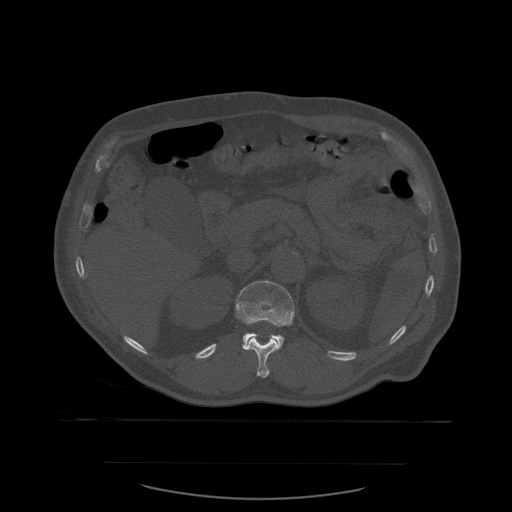
CT including the spine, one axial slice. Position 260 of 590 along the scan axis. Bone window (W 1800 / L 400 HU). 512 × 512 image matrix, field of view 479 × 479 mm. Patient age 71 years. From the clinical record (not read from this slice): primary cancer: lung.
Annotated regions visible in this slice (semi-automatically segmented with operator editing):
- L1 vertebra: bounding box <236,281,295,346> (left, top, right, bottom; pixels)
- T12 vertebra: <242,320,282,378>